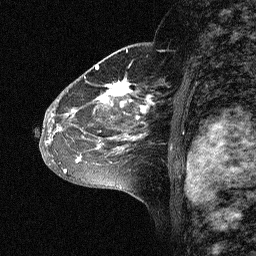
Breast MRI (dynamic contrast-enhanced), one sagittal slice. Position 40 of 64 along the scan axis. Dynamic contrast-enhanced study with each time point stored as its own series, time point 2 of 3 at this slice position (early post-contrast, ordered by acquisition time). 1.5 T. TE 4.5 ms, TR 11 ms. 2.06 mm slice thickness. 256 × 256 image matrix. Patient: female, 46 years. Case-level facts recorded for this patient, not image findings: setting: breast cancer imaged before/during neoadjuvant chemotherapy; receptor status: HER2-positive.
Structures marked on this image (semi-automatically segmented with operator editing):
- analysis volume of interest (the breast-tissue region the enhancement analysis was run in; not a lesion): bounding box <43,72,164,177> (left, top, right, bottom; pixels)
- tumour enhancement mask (voxels above the 90 % enhancement threshold inside the analysis volume of interest): <48,79,155,173>